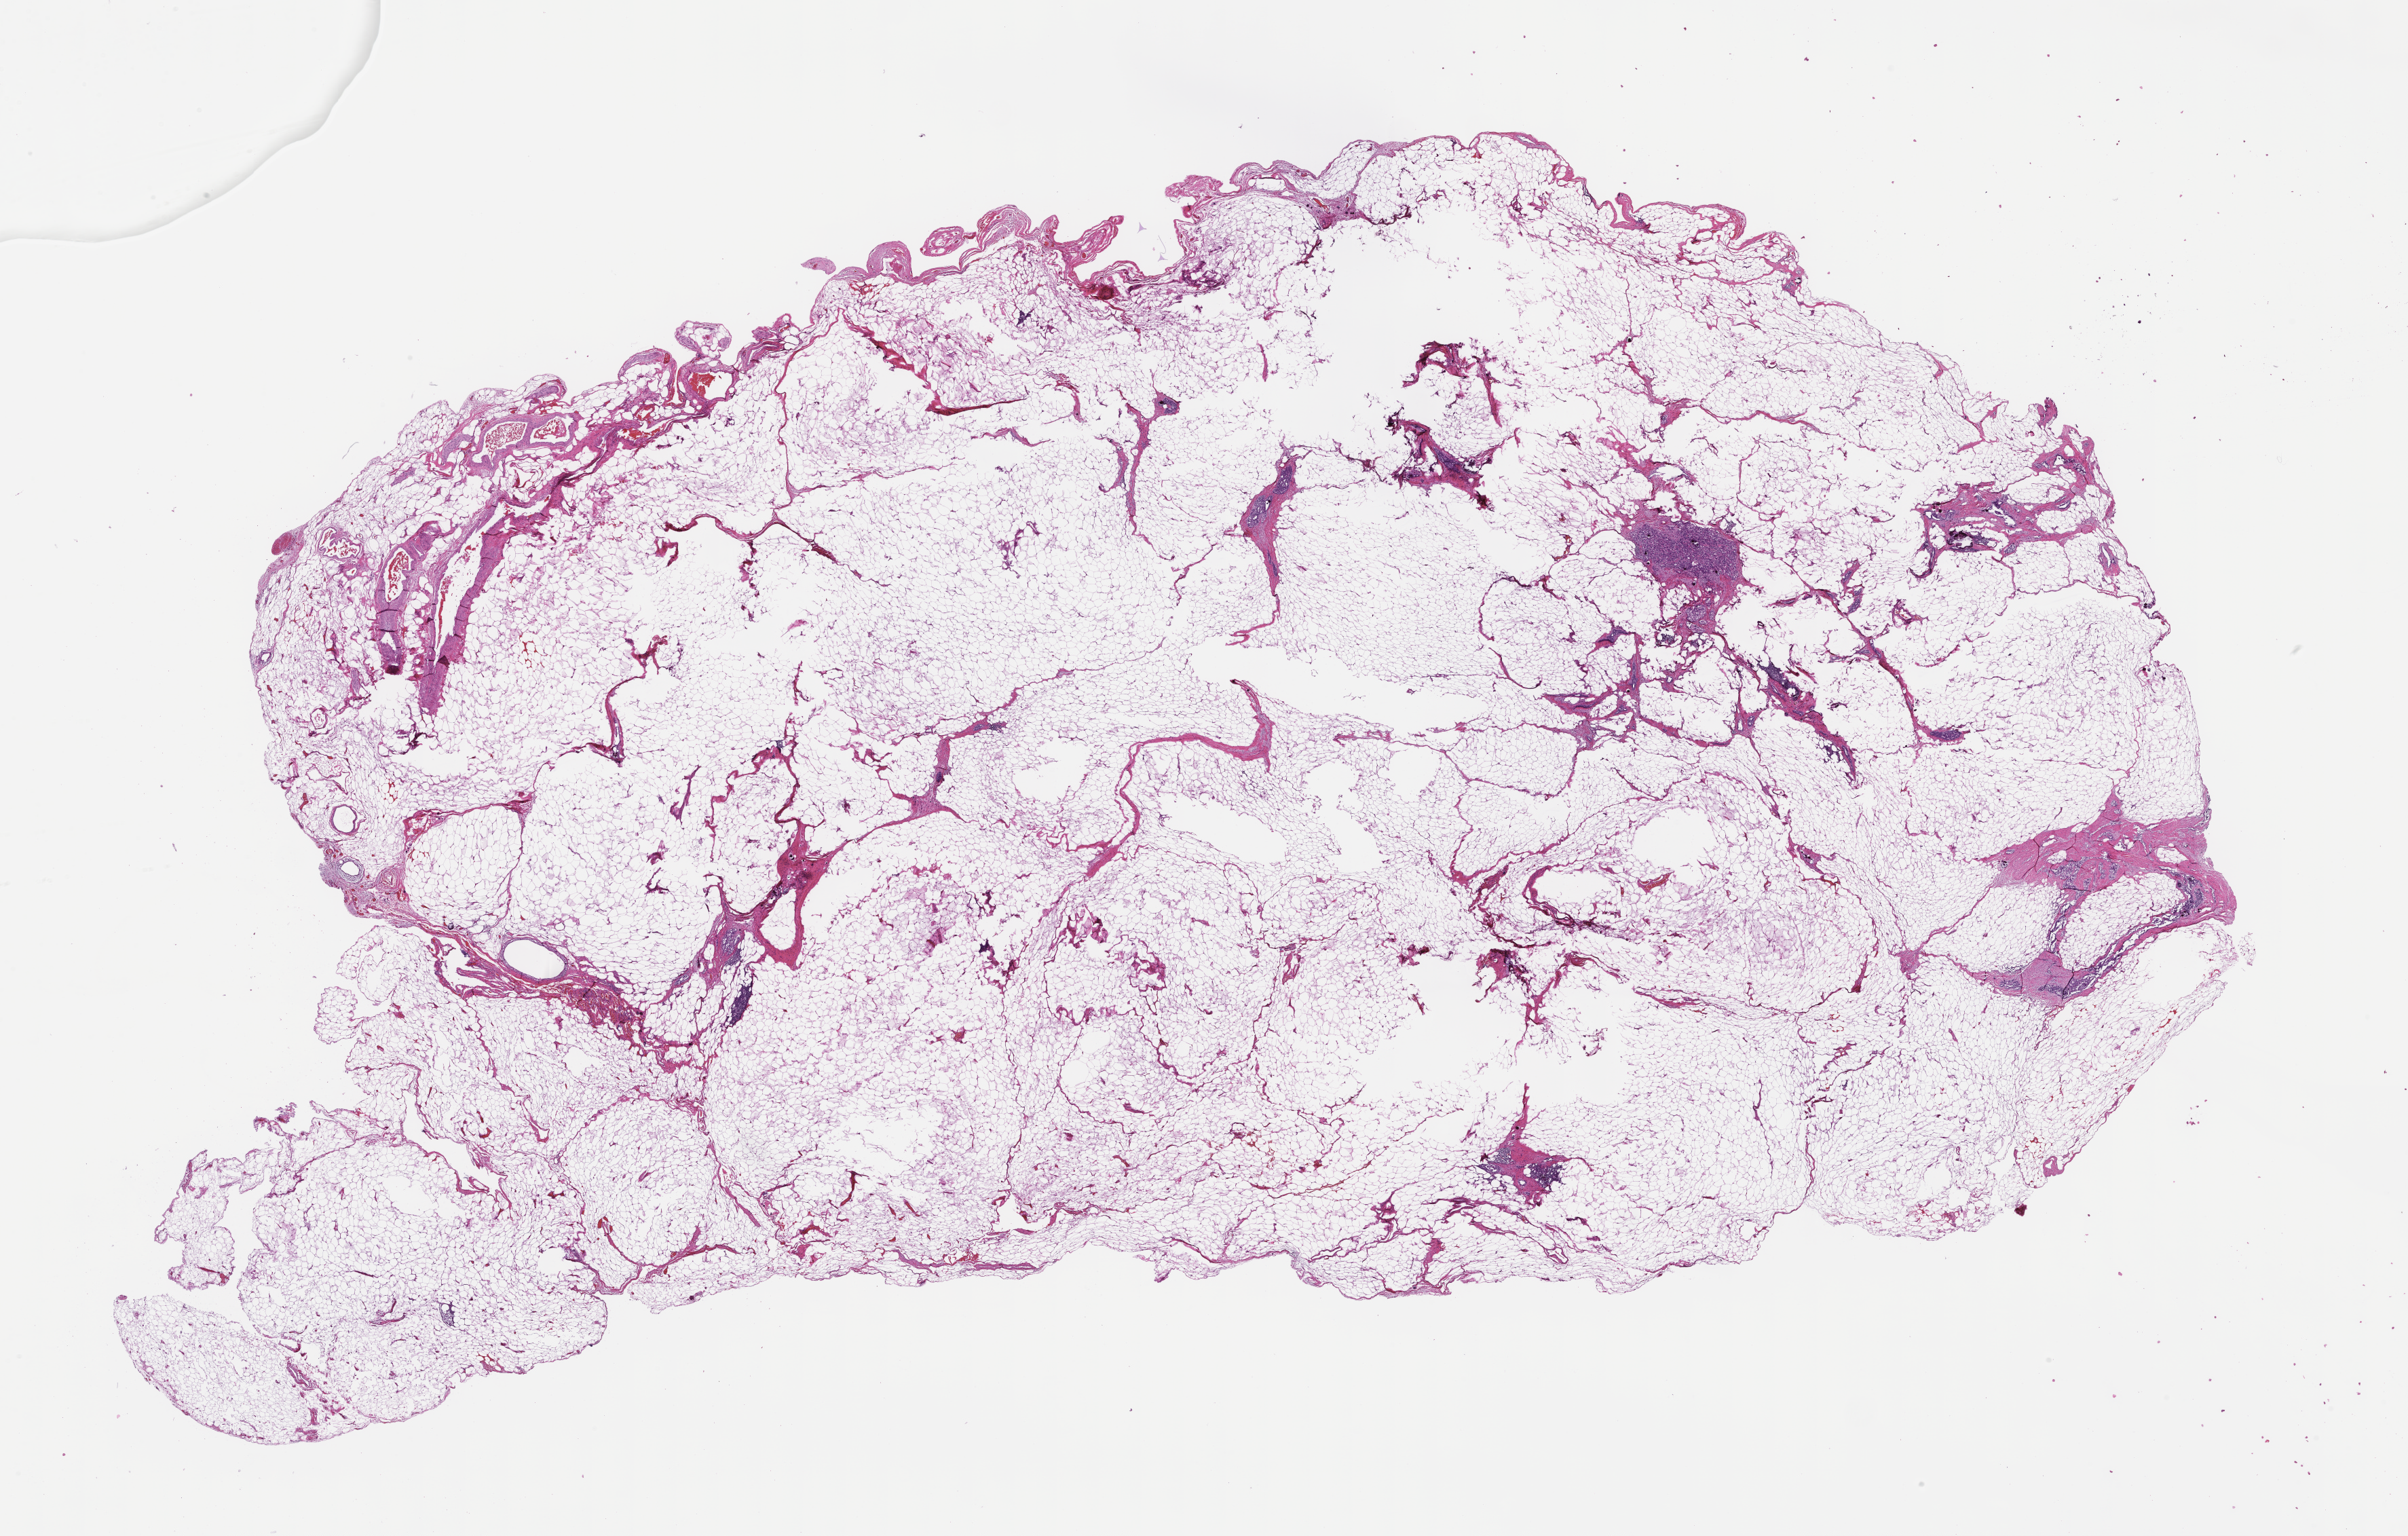
Digitized haematoxylin and eosin-stained section, a low-resolution overview of the entire scanned area, about 28.6 x 18.3 mm. Formalin-fixed, paraffin-embedded (FFPE) tissue. Specimen time point: collected at baseline (before treatment). Patient sex: female.
This section: metastatic tumor tissue. Primary diagnosis of the patient: Ovarian Carcinoma.